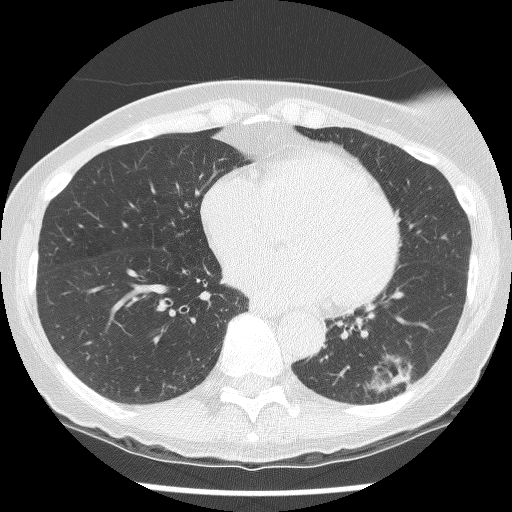
Chest CT (low-dose screening protocol), one axial image. Second screening round (one year after baseline). Lung window (W 1500 / L -600 HU). 2.5 mm slice thickness. Lung (sharp) reconstruction kernel (BONE). 120 kVp. Female participant, aged 61 years at enrolment. Current smoker at enrolment.
Expert reader's lesion annotation, box from (x=335, y=335) to (x=435, y=418) px. The screening reader recorded 2 non-calcified nodules or masses ≥4 mm on this exam (left lower lobe, left lower lobe); which of them this box marks is not recorded. Official screen result: positive, no significant change: stable abnormalities potentially related to lung cancer, unchanged since the prior screening exam. Lung cancer was diagnosed 585 days after this screen (after the third annual screen): non-small cell carcinoma, left lower lobe, poorly differentiated (G3), stage IB (AJCC 6th edition), 100 mm at pathology.